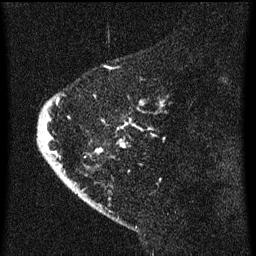
Breast MRI (dynamic contrast-enhanced), one sagittal slice; slice 14 of 60 in the series (ordered by position); dynamic contrast-enhanced series, image 2 of 3 at this slice position (ordered by acquisition); 1.5 T; TE 4.2 ms, TR 8 ms; 2 mm slice thickness; 256 × 256 image matrix, field of view 180 × 180 mm. Patient: female, 47 years.
Annotated regions visible in this slice (semi-automatic segmentation, software-assisted and operator-edited):
- analysis volume of interest (the breast-tissue region the enhancement analysis was run in; not a lesion): bounding box <38,78,164,193> (left, top, right, bottom; pixels)
- tumour enhancement mask (voxels above the 70 % enhancement threshold inside the analysis volume of interest): <38,94,164,183>